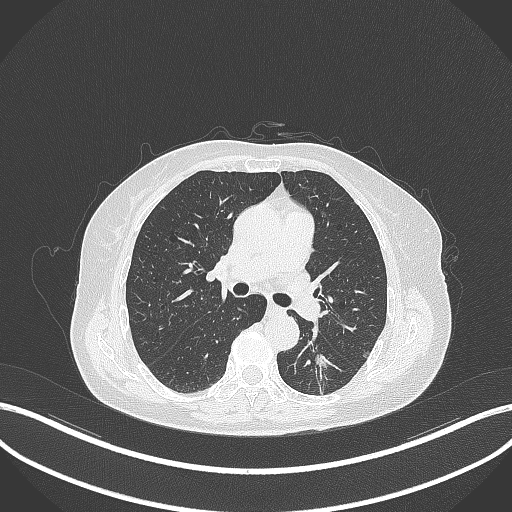
Chest CT, one axial slice. Position 175 of 352 along the scan axis. 120 kVp. Lung window (W 1500 / L -600 HU). 1 mm slice thickness. 512 × 512 image matrix, field of view 400 × 400 mm. Female patient, age 70 years. Case-level facts recorded for this patient, not image findings: clinical TNM (as recorded): T1c N0 M0.
Annotated regions visible in this slice (rectangle marked by the reading radiologist):
- lung tumour (recorded histology: adenocarcinoma): box from (x=308, y=350) to (x=334, y=379) px